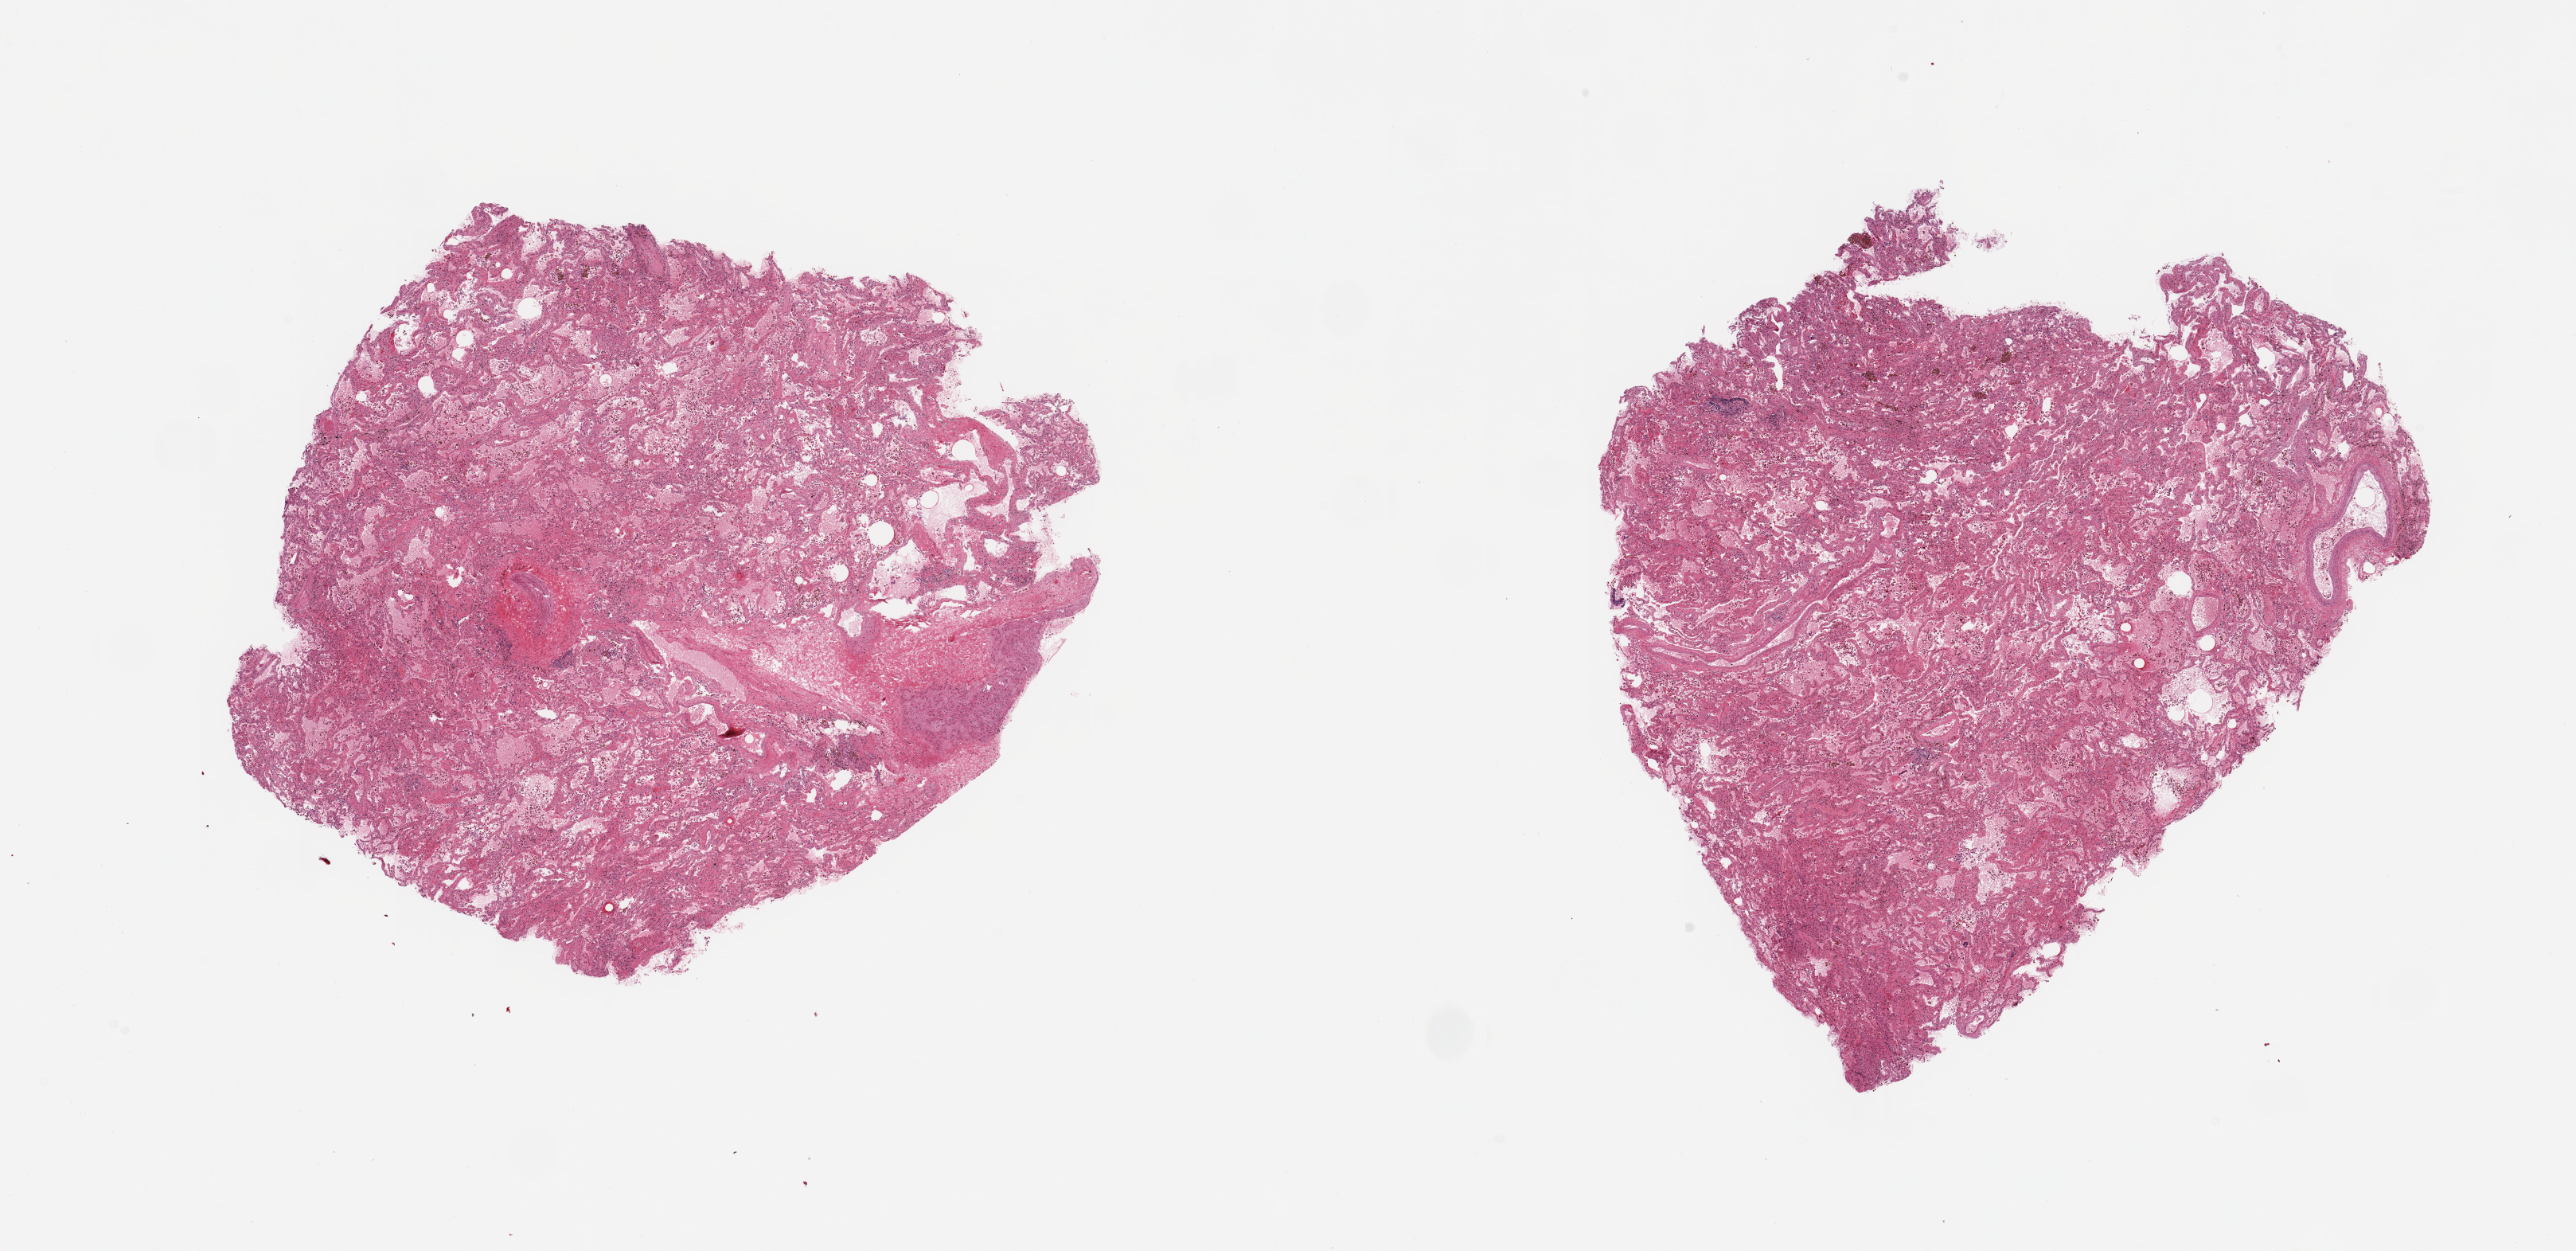
Whole-slide image, H&E stain, shown as a low-resolution overview of the whole scanned area (about 25.6 x 12.4 mm, from a 20x scan). PAXgene-fixed, paraffin-embedded tissue. Sampled site (target tissue): lung. Donor tissue sample. Donor: female.
Reviewer comment on this tissue sample: 2 pieces, moderate congestion/edema.